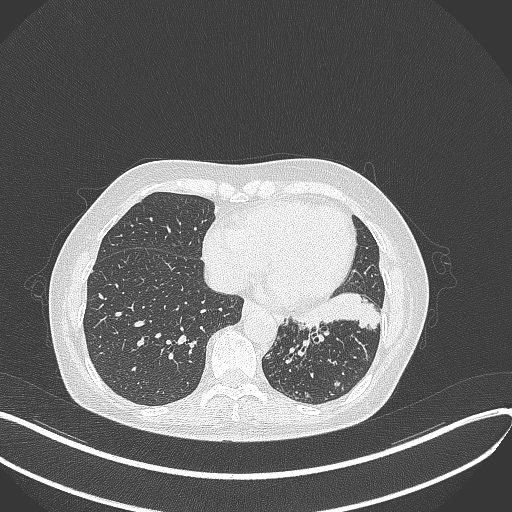
Chest CT, one axial slice; position 133 of 429 along the scan axis; reconstruction kernel B70f; lung window (W 1500 / L -600 HU); 1 mm slice thickness; 512 × 512 image matrix, field of view 400 × 400 mm. Patient: female, 63 years. Case-level facts recorded for this patient, not image findings: clinical TNM (as recorded): T1b N0 M0; histopathological grade: G2-3.
Outlined on this slice (rectangle marked by the reading radiologist):
- lung tumour (recorded histology: adenocarcinoma): bounding box [x1, y1, x2, y2] px = [292, 293, 381, 336]